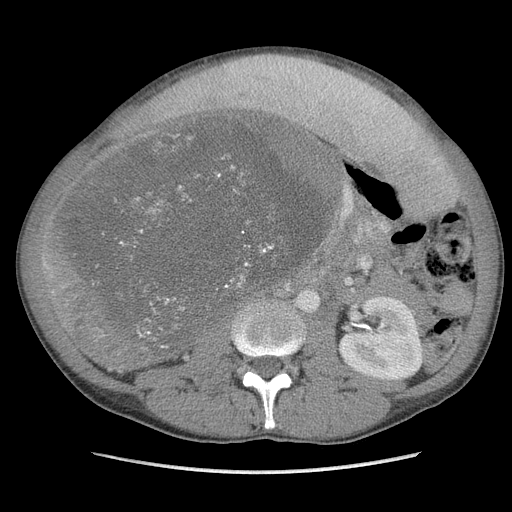
Contrast-enhanced abdominal CT, one axial slice. Slice 54 of 115 in the series (ordered by position). Soft-tissue window (W 400 / L 40 HU). 512 × 512 image matrix. Male patient. Case-level facts recorded for this patient, not image findings: diagnosis: adrenocortical carcinoma; tumour side: right adrenal; Ki-67 index: 13 %; stage (as recorded): 3.
Outlined on this slice (semi-automatic segmentation, software-assisted and operator-edited):
- mass: bounding box <57,112,332,367> (left, top, right, bottom; pixels)